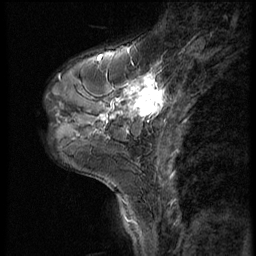
Breast MRI (dynamic contrast-enhanced), one sagittal slice; position 19 of 56 along the scan axis; 3 images stored at this slice position (order not interpretable as contrast timing); 1.5 T; TE 4.2 ms, TR 9 ms; 2.5 mm slice thickness; 256 × 256 image matrix, field of view 180 × 180 mm. Patient: female, 46 years. Case-level facts recorded for this patient, not image findings: setting: breast cancer imaged before/during neoadjuvant chemotherapy; receptor status: HER2-positive.
Outlined on this slice (semi-automatically segmented with operator editing):
- analysis volume of interest (the breast-tissue region the enhancement analysis was run in; not a lesion): box from (x=79, y=68) to (x=190, y=143) px
- tumour enhancement mask (voxels above the 140 % enhancement threshold inside the analysis volume of interest): (x=100, y=73)–(x=166, y=123)